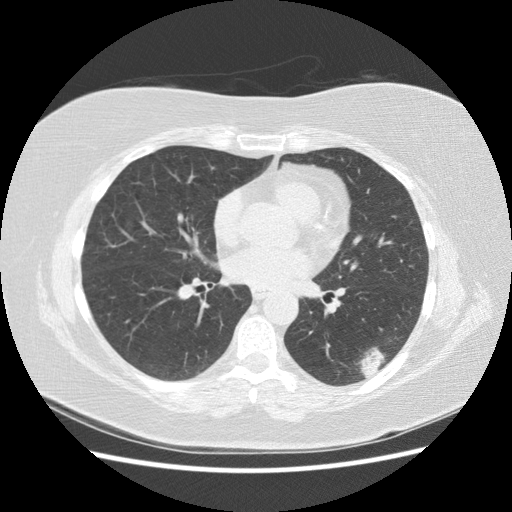
Axial slice from a low-dose chest CT screening exam. Third screening round (two years after baseline). Lung window (W 1500 / L -600 HU). 2.5 mm slice thickness. Female, age 57 years at enrolment. Current smoker at enrolment.
- Lesion marked by an expert reader, bounding box [x1, y1, x2, y2] px = [337, 324, 406, 388].
- Screening reader's record for this exam (one nodule recorded; not confirmed to be the boxed lesion): non-calcified nodule or mass ≥4 mm, left lower lobe, 40 × 20 mm, poorly defined margins, mixed attenuation, pre-existing on the prior screen: yes; interval growth: yes.
- Lung cancer was diagnosed 55 days after this screen: squamous cell carcinoma, NOS, left lower lobe, poorly differentiated (G3), stage IB (AJCC 6th edition), 40 mm at pathology.